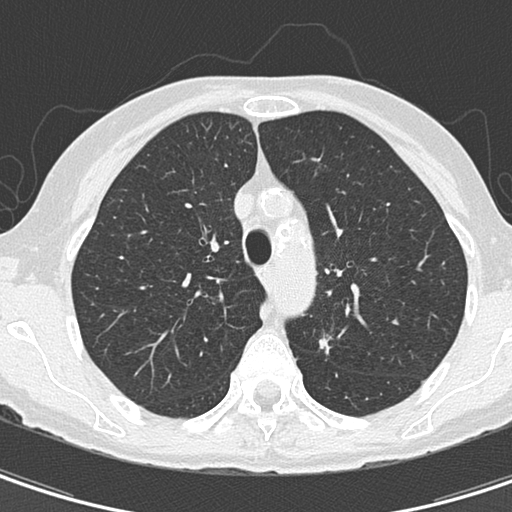
Chest CT (low-dose screening protocol), one axial image; baseline annual screen; lung window (W 1500 / L -600 HU); 2 mm slice thickness; slice 45 of 157 in the series. Female participant, aged 67 years at enrolment. Current smoker at enrolment.
- Expert-annotated lung lesion, bounding box <300,321,355,368> (left, top, right, bottom; pixels).
- Screening reader's record for this exam (one nodule recorded; not confirmed to be the boxed lesion): non-calcified nodule or mass ≥4 mm, left upper lobe, 11 × 8 mm, spiculated (stellate) margins, soft tissue attenuation.
- Later outcome: lung cancer diagnosed 73 days after this screen — adenocarcinoma, NOS, left upper lobe, poorly differentiated (G3), stage IA (AJCC 6th edition), 13 mm at pathology.